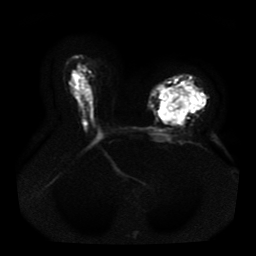
Breast MRI, one axial slice. Slice 26 of 41 in the series (ordered by position). Diffusion-weighted series; image 2 of 4 stored at this slice position (different b-values; order by instance number). 1.5 T. 5 mm slice thickness. 256 × 256 image matrix. Female patient.
Annotated regions visible in this slice (manually delineated by an expert):
- tumour on diffusion-weighted imaging: box from (x=160, y=83) to (x=205, y=122) px